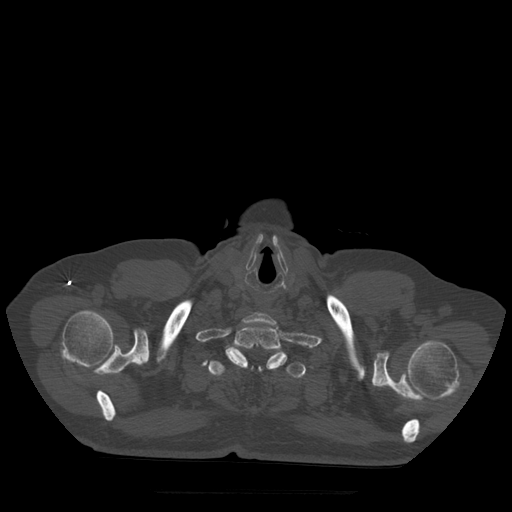
CT including the spine, one axial slice. Slice 437 of 522 in the series (ordered by position). Bone window (W 1800 / L 400 HU). 512 × 512 image matrix, field of view 420 × 420 mm. Patient age 72 years. From the clinical record (not read from this slice): primary cancer: prostate.
Structures marked on this image (semi-automatically segmented with operator editing):
- T1 vertebra: bounding box [x1, y1, x2, y2] px = [225, 322, 288, 370]
- T2 vertebra: [208, 350, 306, 379]